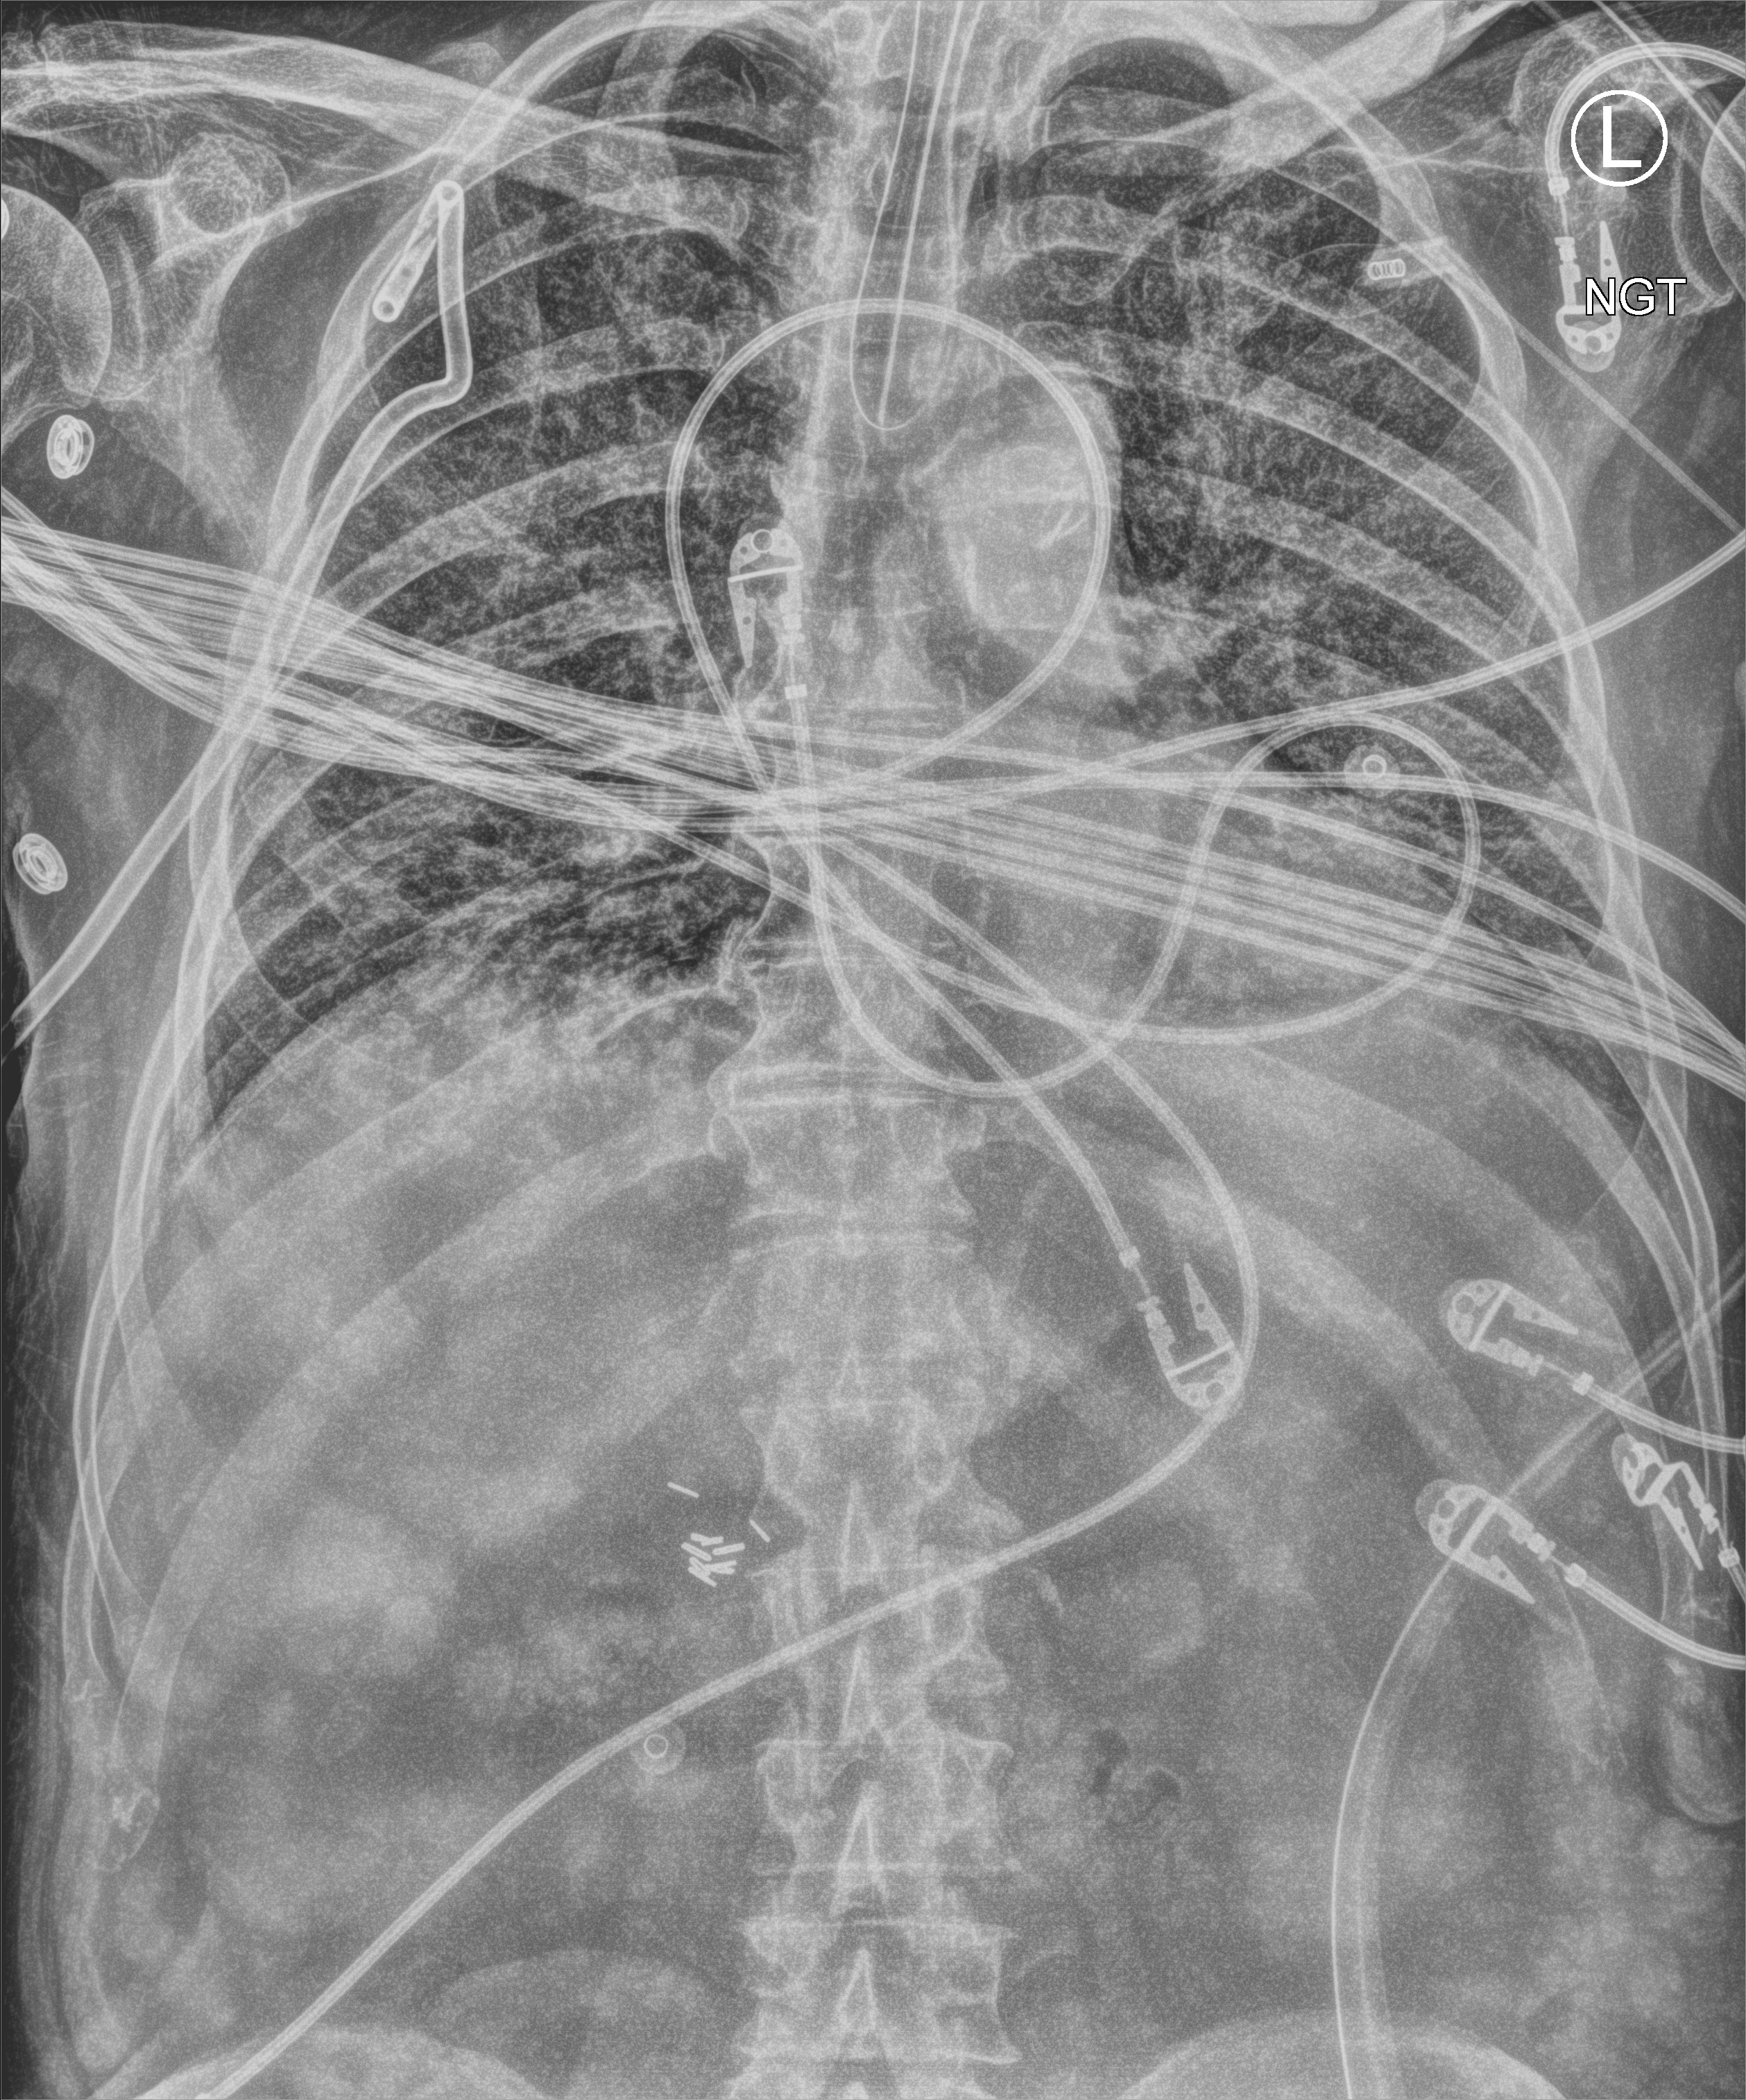
Bedside chest radiograph (computed radiography); anteroposterior (AP) projection. Patient hospitalised with COVID-19; male, aged 75–90 years.
Admission-level facts for this patient (not findings on this image; timing relative to this image not recorded): mechanically ventilated during this hospital stay: yes.